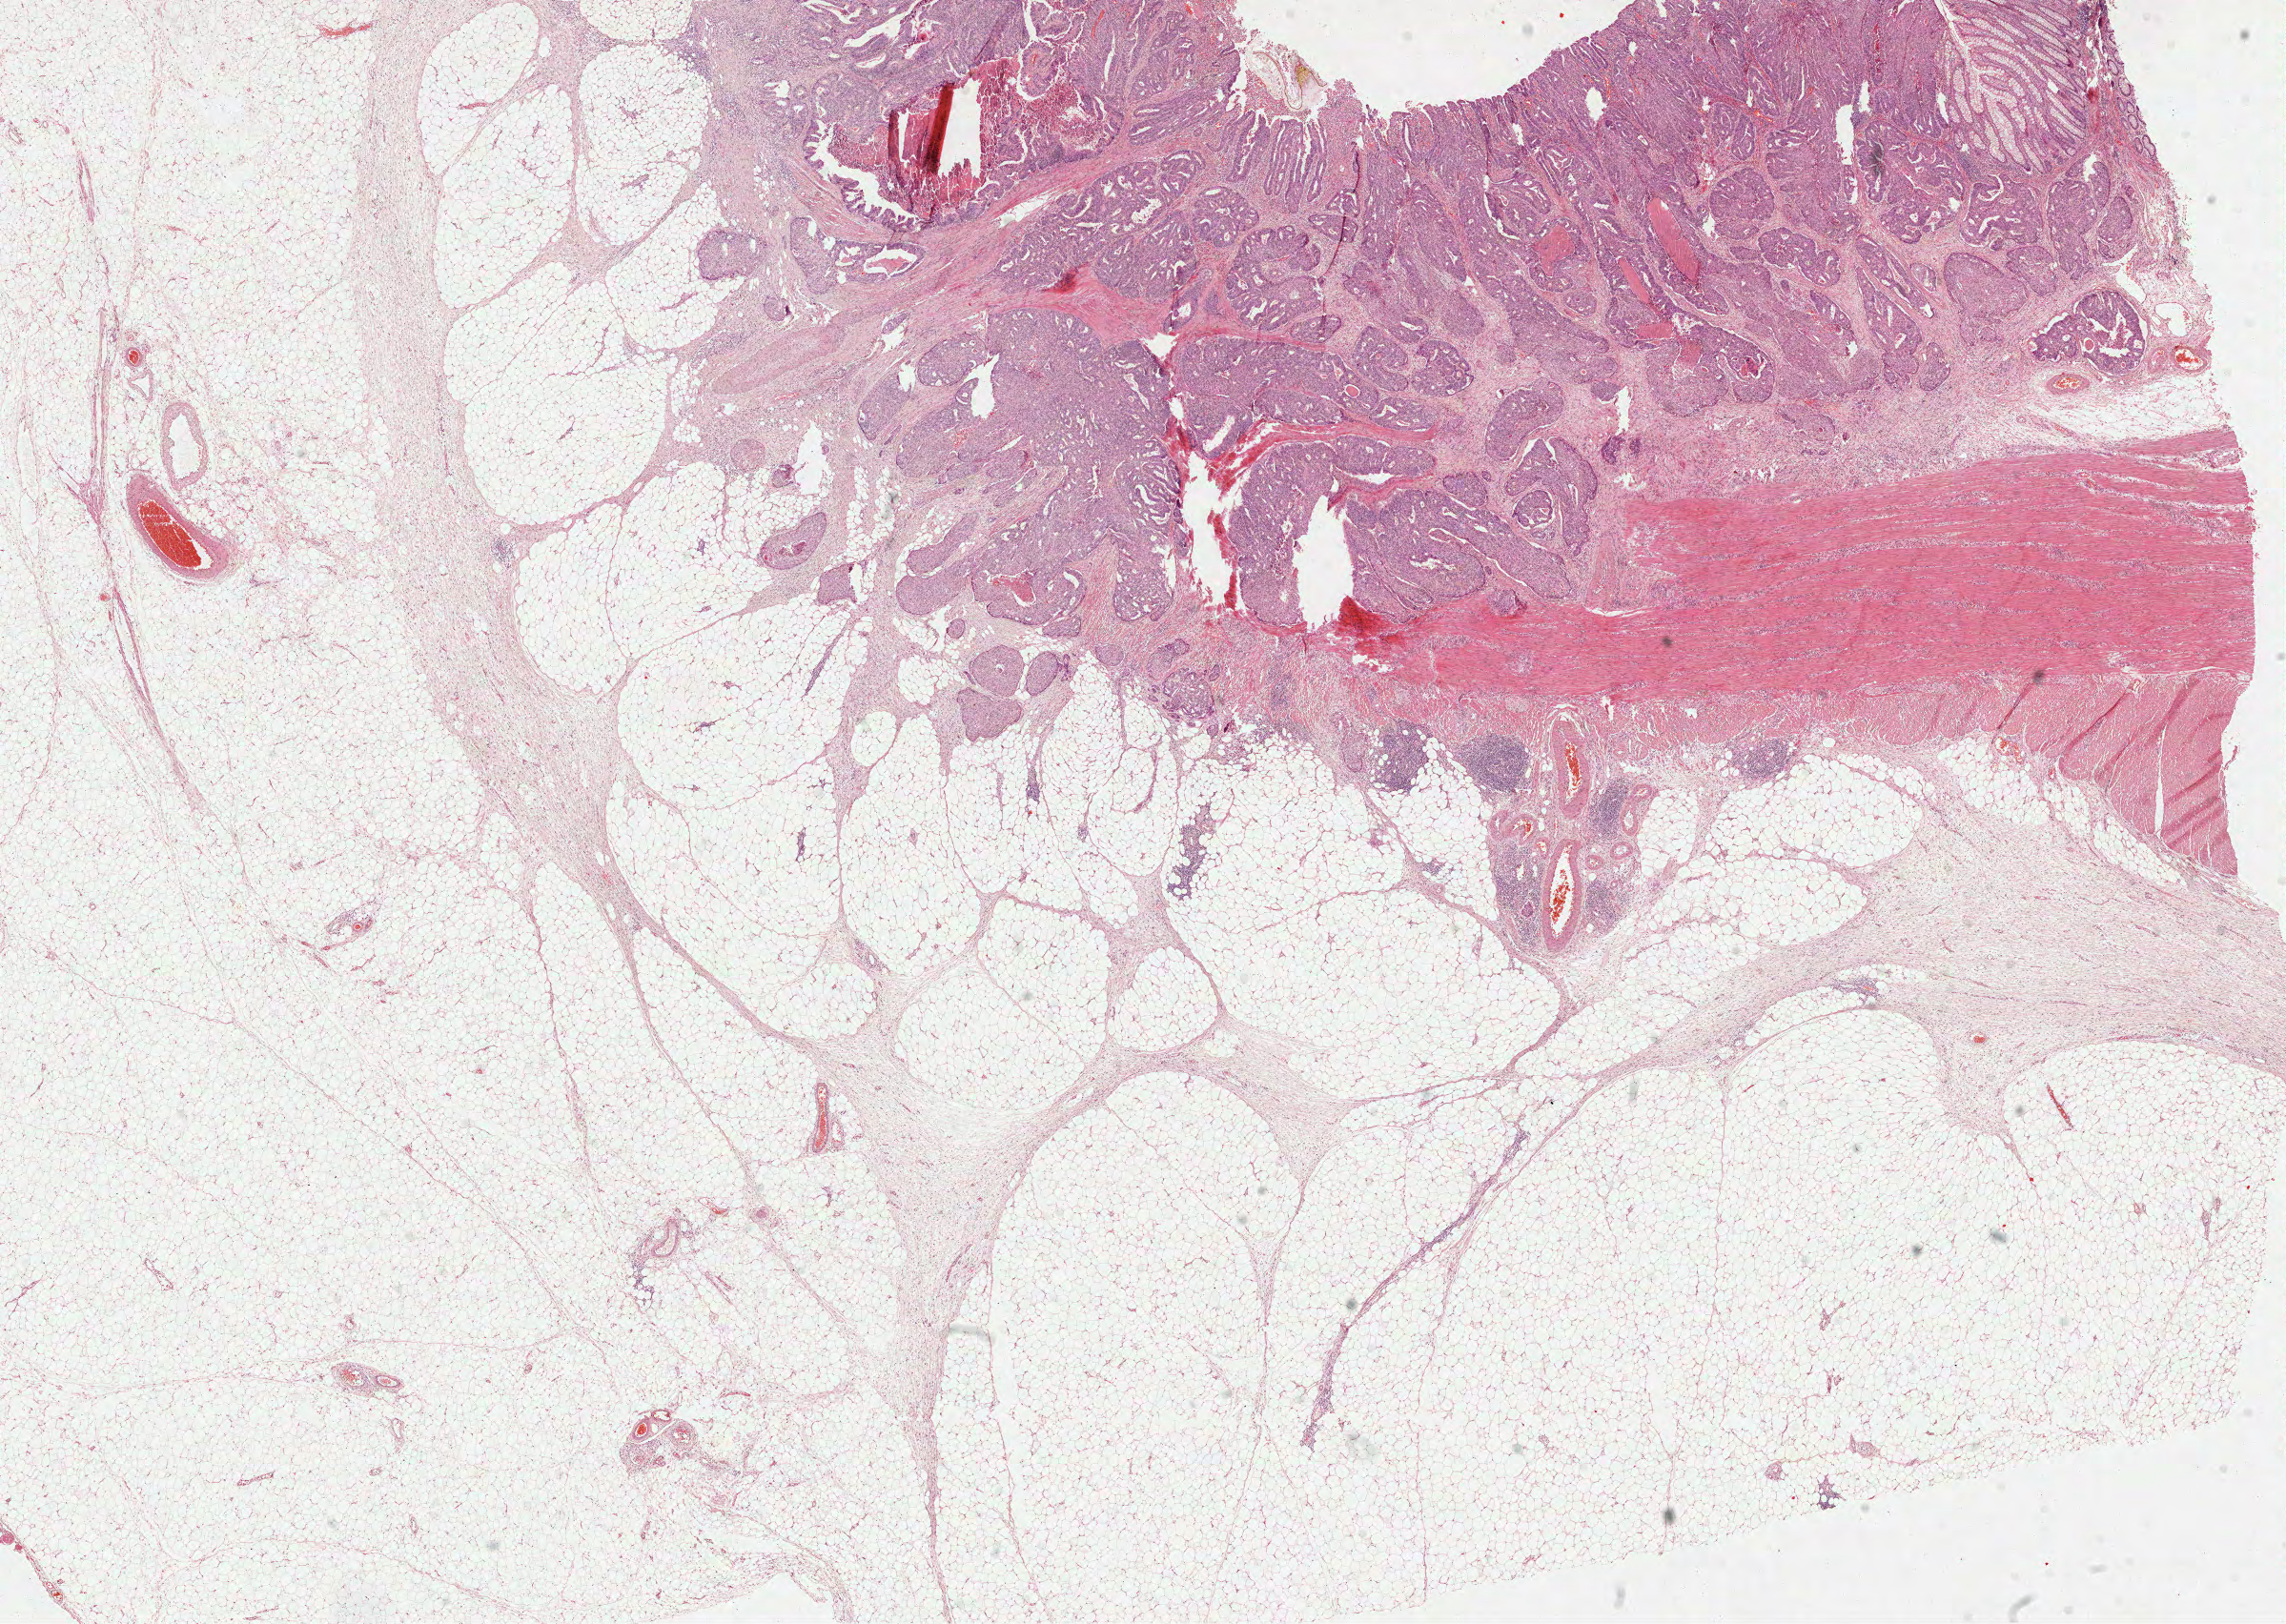
Digitized H&E-stained tissue section (whole slide) — shown as a low-resolution overview of the whole scanned area (about 19.3 x 13.7 mm, from a 40x scan), FFPE section, rectum, primary tumour sample. Male patient; age at initial diagnosis 53 years.
* AJCC pathologic stage: IIIC
* pathologic diagnosis: Adenocarcinoma in tubulovillous adenoma